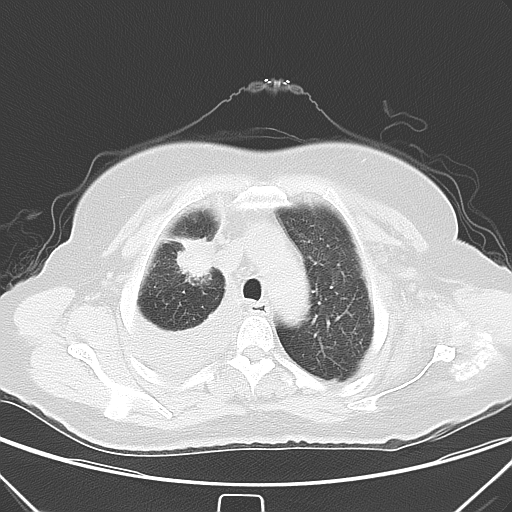
Chest CT, one axial slice. Slice 45 of 55 in the series (ordered by position). 120 kVp. Lung window (W 1500 / L -600 HU). 5 mm slice thickness. 512 × 512 image matrix, field of view 352 × 352 mm. Patient: female, 66 years. From the clinical record (not read from this slice): clinical TNM (as recorded): T2 N0 M1.
Outlined on this slice (rectangle marked by the reading radiologist):
- lung tumour (recorded histology: adenocarcinoma): bounding box (x1, y1, x2, y2) in pixels: (177, 230, 214, 283)